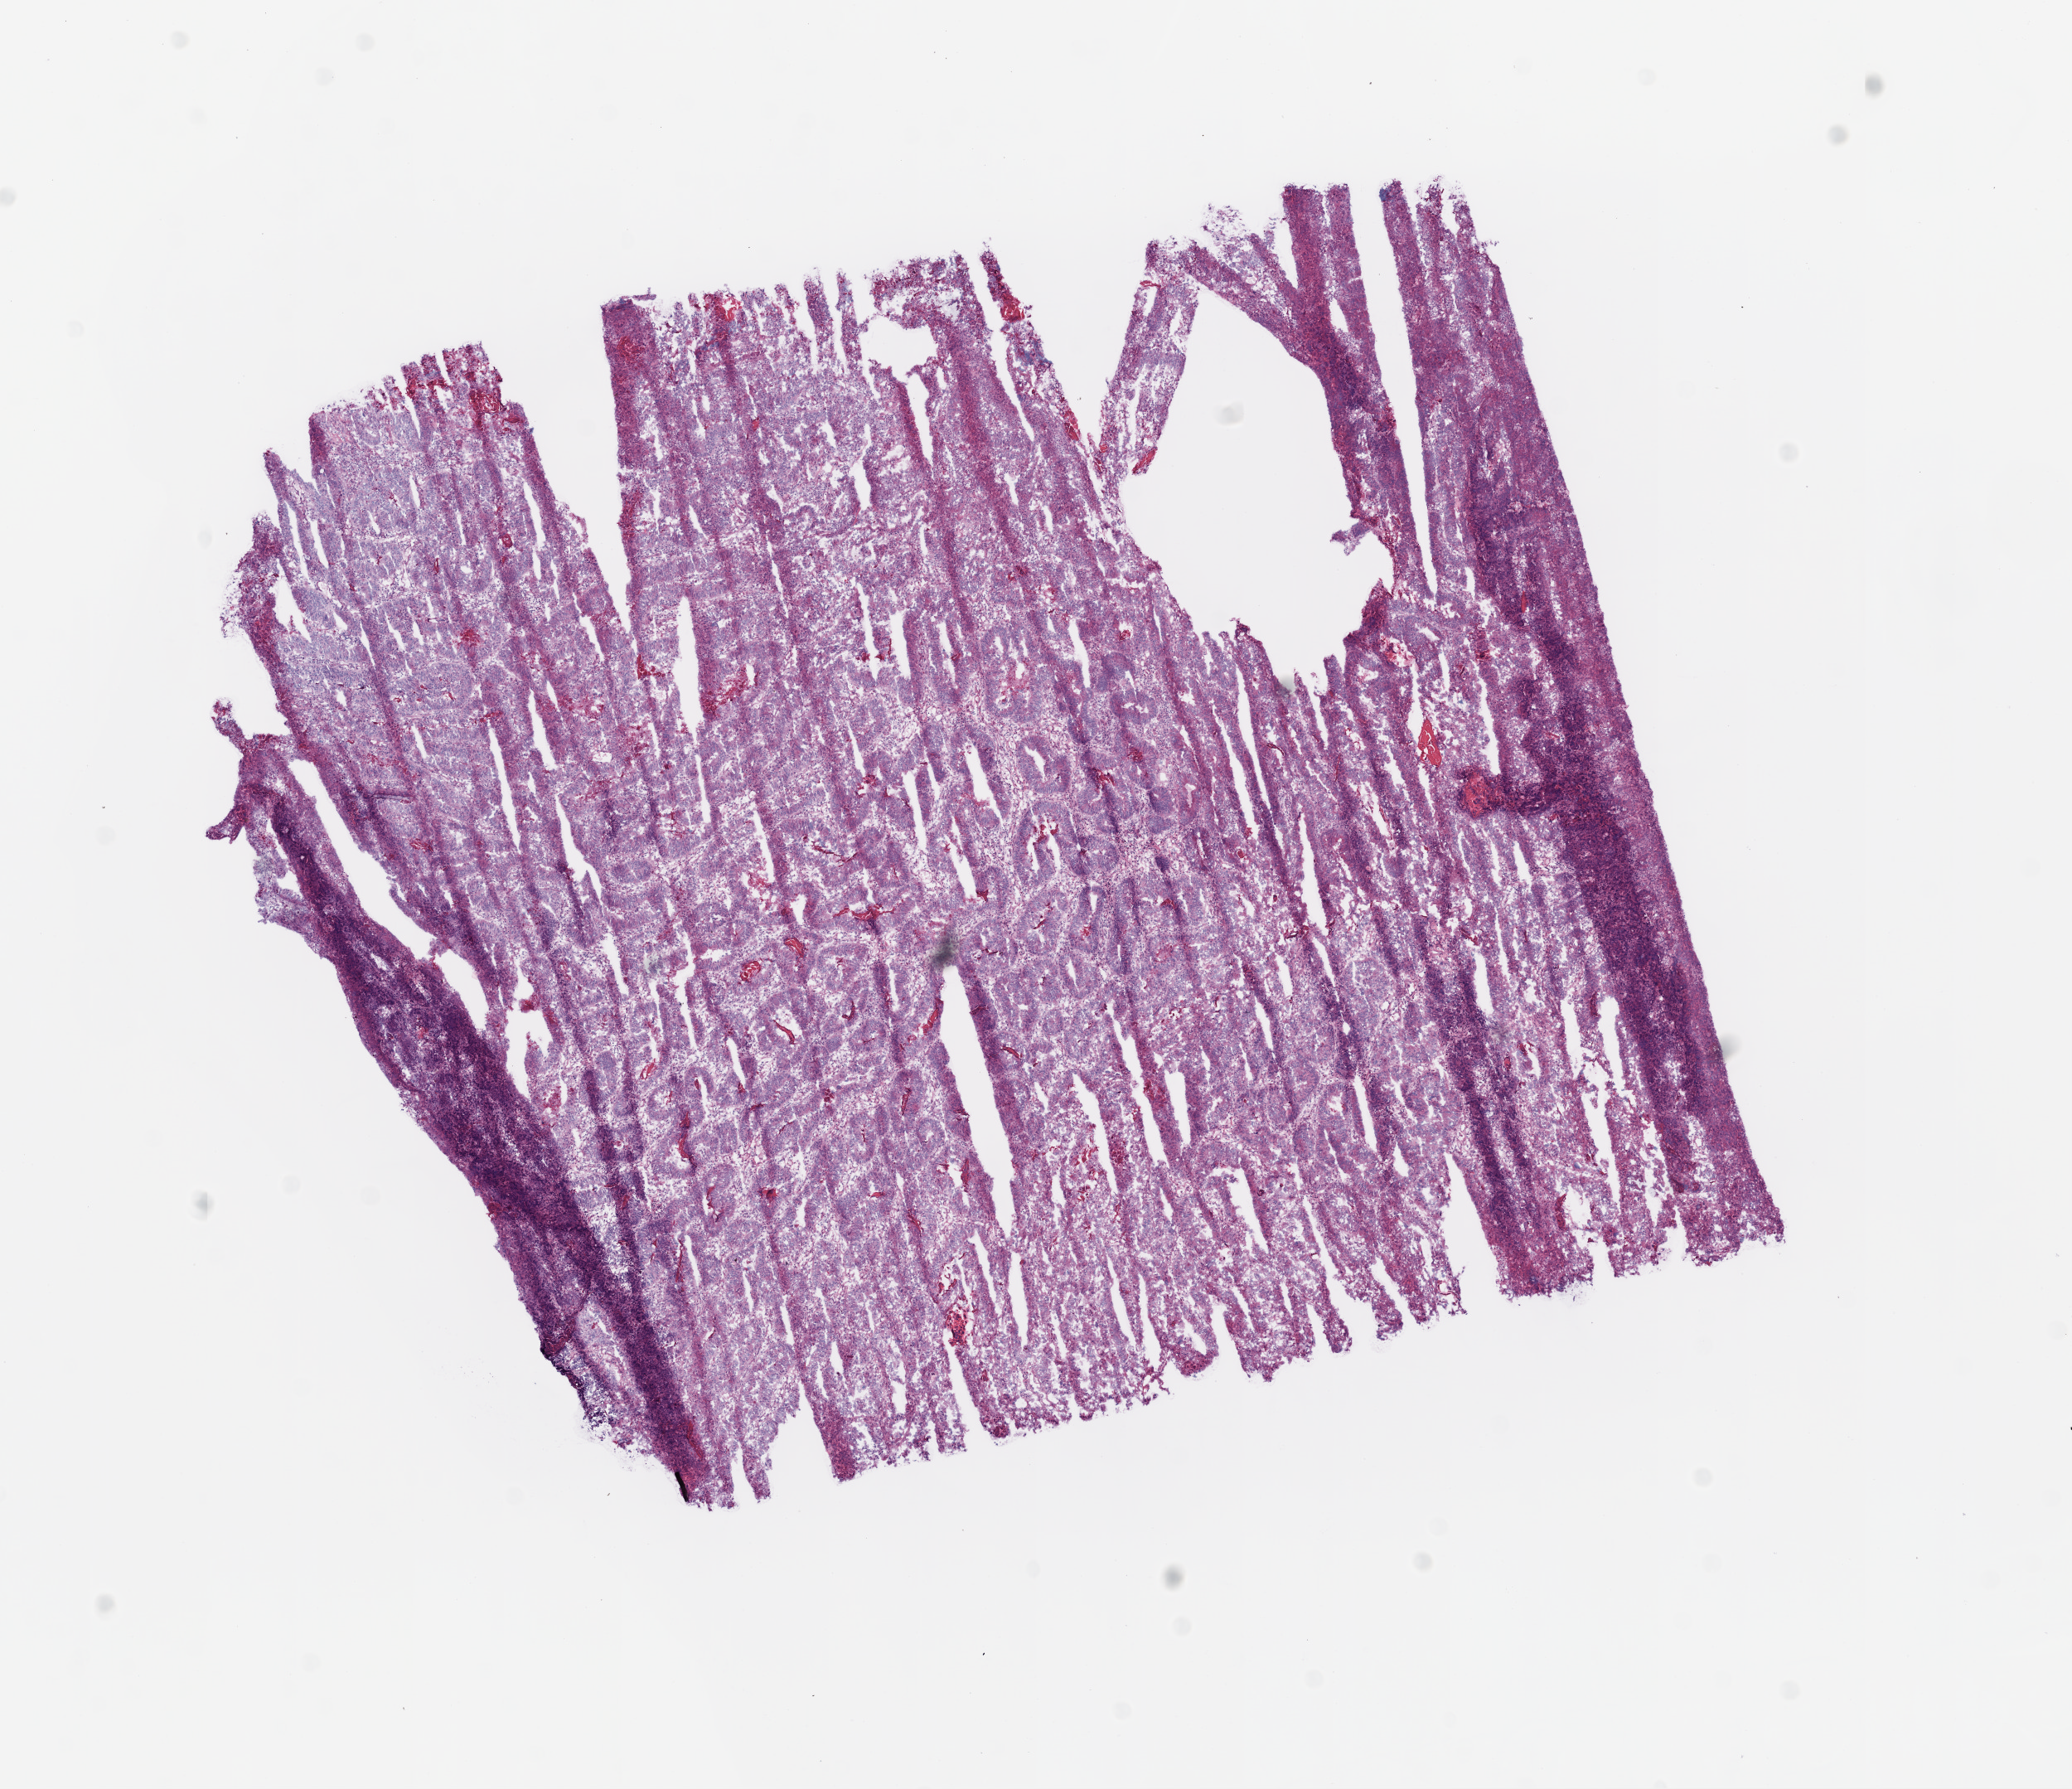
H&E-stained whole-slide image — shown as a low-resolution overview of the whole scanned area (about 10.0 x 8.7 mm, from a 20x scan); frozen section from the top of the tissue portion; rectum, primary tumour sample. Female, age 72 years at initial diagnosis. Slide review estimates, as recorded: tumour cells 95%, tumour nuclei 90%, normal cells 0%, stromal cells 5%, necrosis 0%. Inflammatory infiltration, as recorded: lymphocyte infiltration 5%.
- AJCC pathologic stage: IIA
- pathologic diagnosis: Adenocarcinoma, NOS
- lymph nodes positive (case pathology): 0 of 38 examined